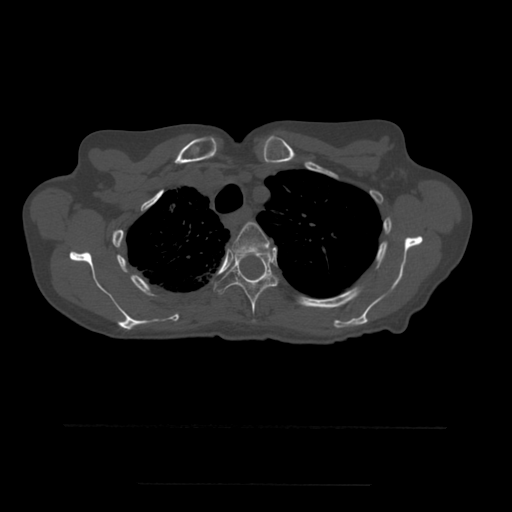
CT including the spine, one axial slice. Slice 411 of 544 in the series (ordered by position). Bone window (W 1800 / L 400 HU). 1.25 mm slice thickness. 512 × 512 image matrix, field of view 350 × 350 mm. Patient age 58 years. Case-level facts recorded for this patient, not image findings: primary cancer: lung.
Structures marked on this image (semi-automatic segmentation, software-assisted and operator-edited):
- T3 vertebra: bounding box <231,222,270,255> (left, top, right, bottom; pixels)
- T4 vertebra: <214,250,278,322>